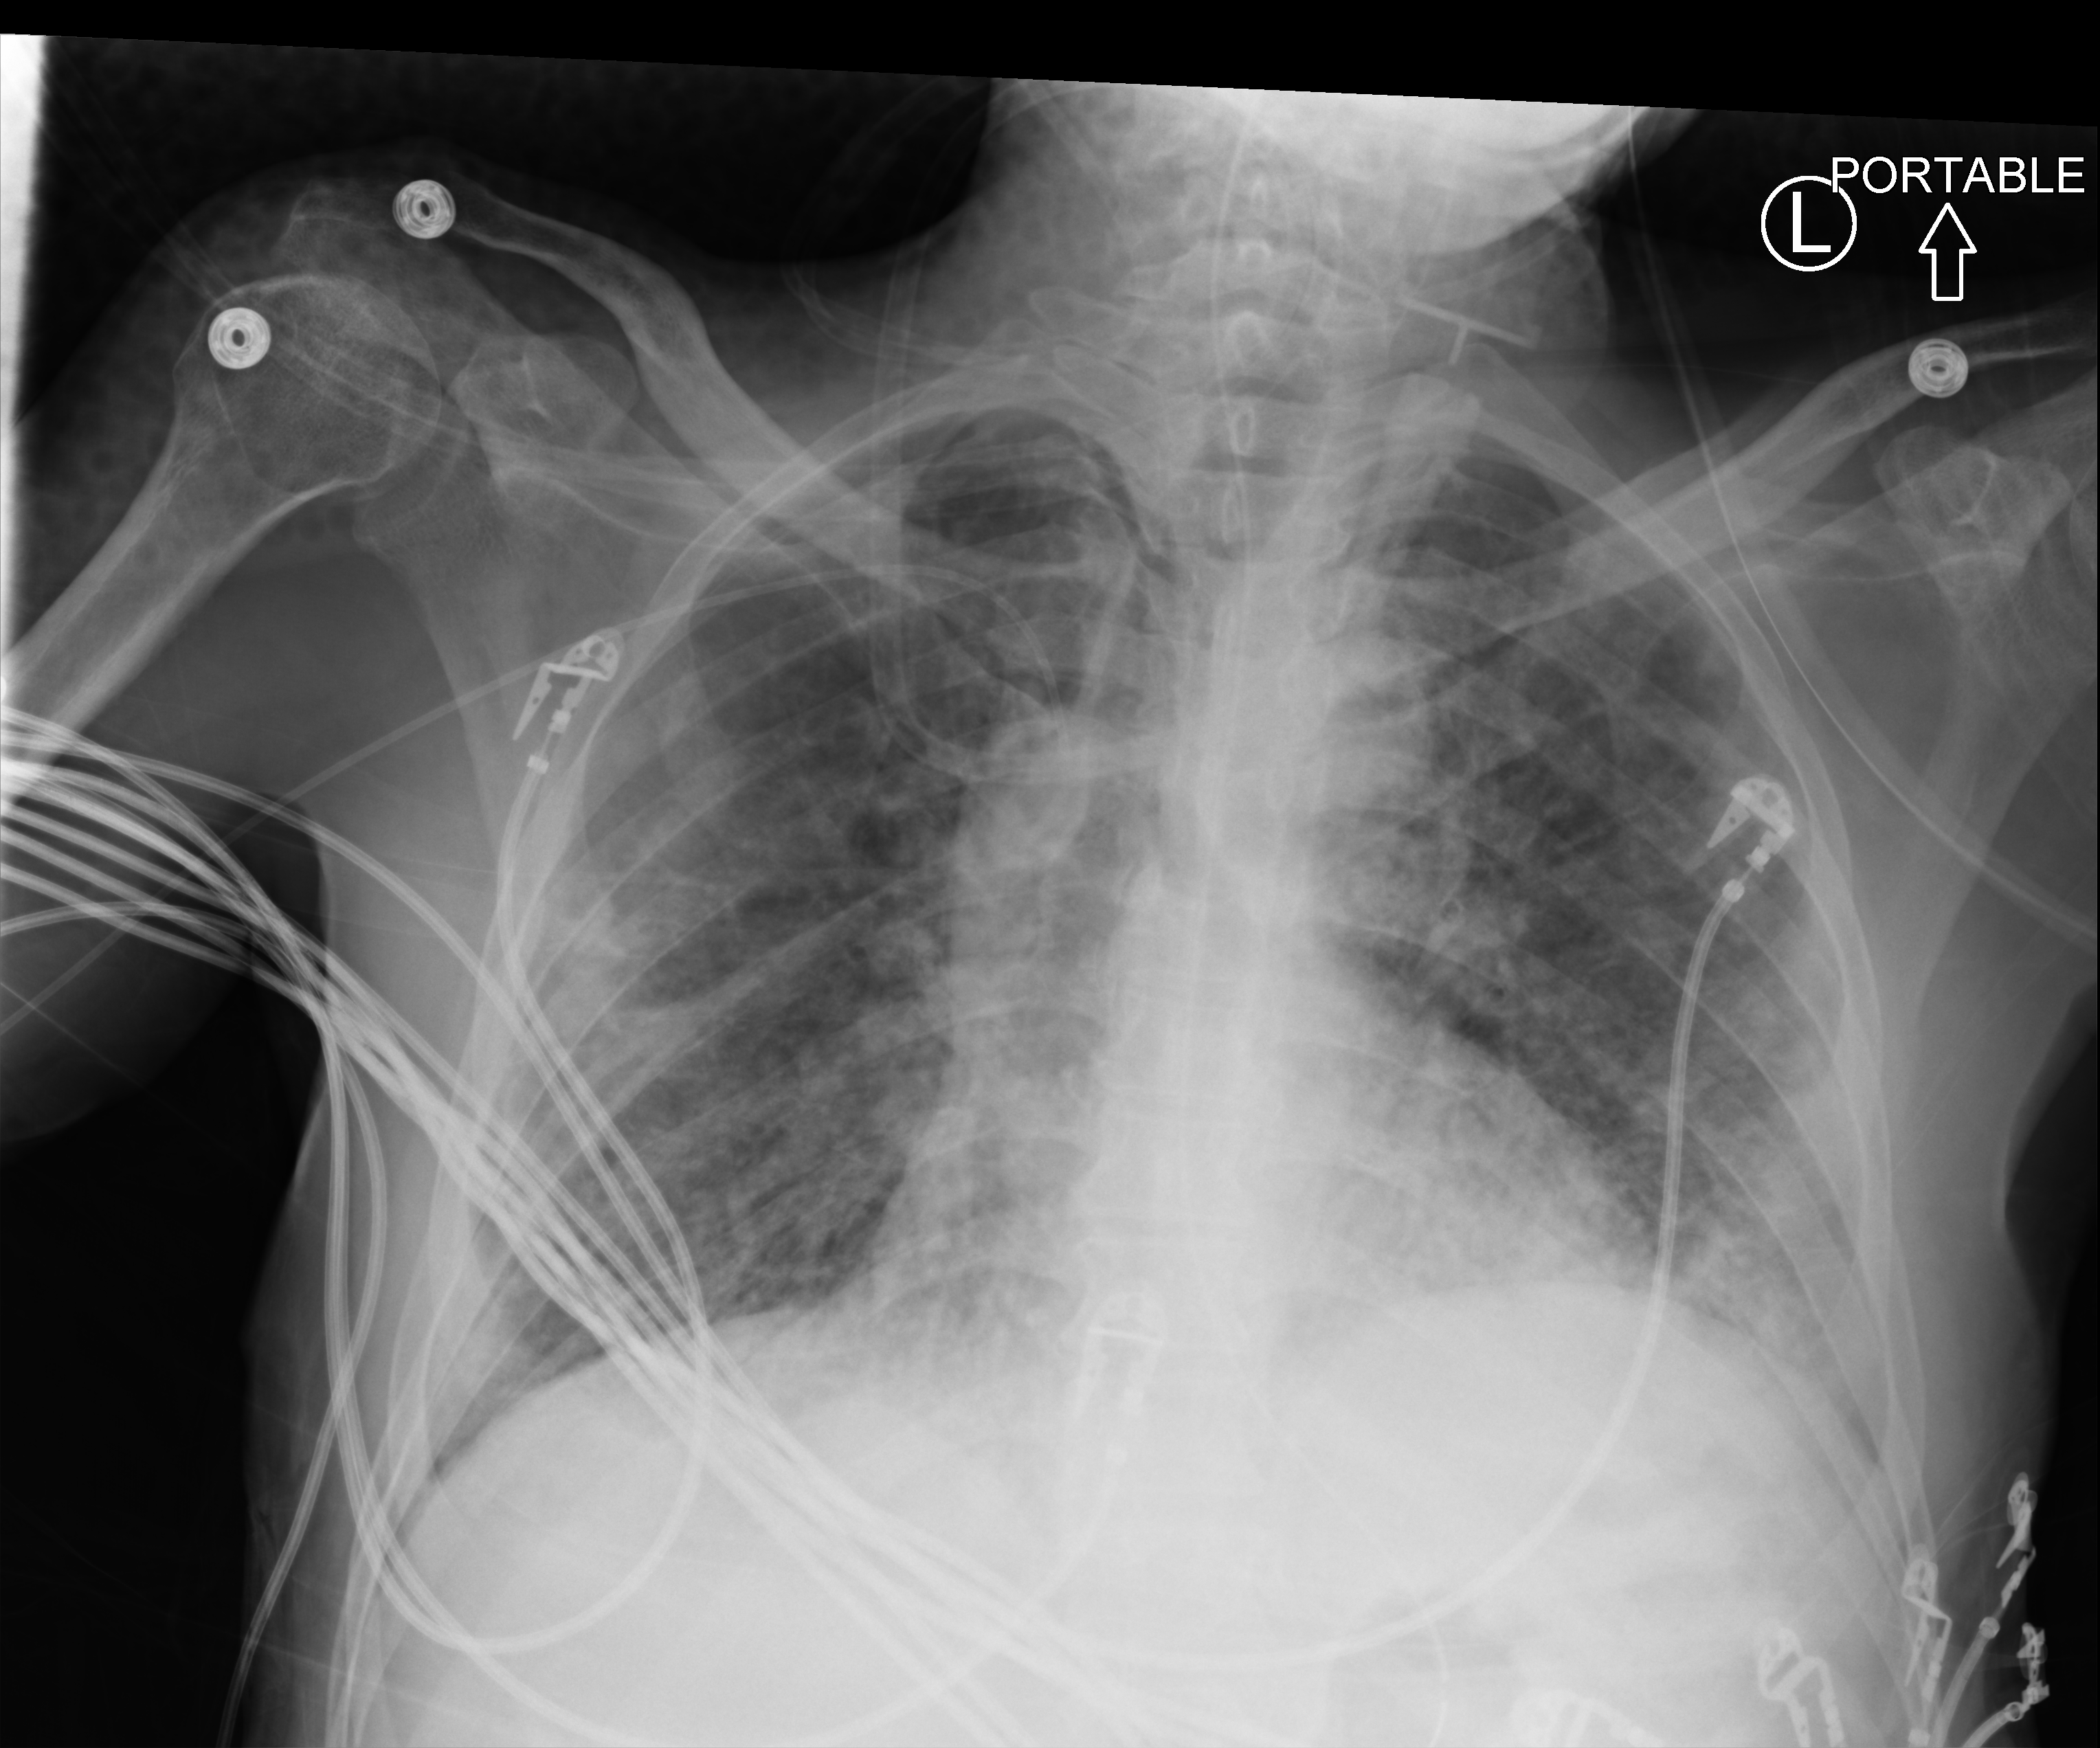
Portable chest radiograph, anteroposterior (AP) projection. Patient hospitalised with COVID-19; male, aged 18–59 years.
Hospital-stay facts (about this admission, not read from this image; timing relative to this image not recorded):
- other chronic lung disease (admission record): no
- mechanically ventilated during this hospital stay: yes